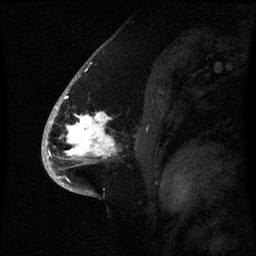
Breast MRI (dynamic contrast-enhanced), one sagittal slice. Slice 42 of 60 in the series (ordered by position). Dynamic contrast-enhanced series, image 2 of 3 at this slice position (ordered by acquisition). 1.5 T. TE 4.2 ms, TR 8.4 ms. 2.1 mm slice thickness. 256 × 256 image matrix. Patient: female, 53 years. From the clinical record (not read from this slice): setting: breast cancer imaged before/during neoadjuvant chemotherapy; receptor status: HR-positive, HER2-negative.
Outlined on this slice (semi-automatic segmentation, software-assisted and operator-edited):
- analysis volume of interest (the breast-tissue region the enhancement analysis was run in; not a lesion): box from (x=52, y=90) to (x=119, y=171) px
- tumour enhancement mask (voxels above the 70 % enhancement threshold inside the analysis volume of interest): (x=52, y=98)–(x=116, y=157)